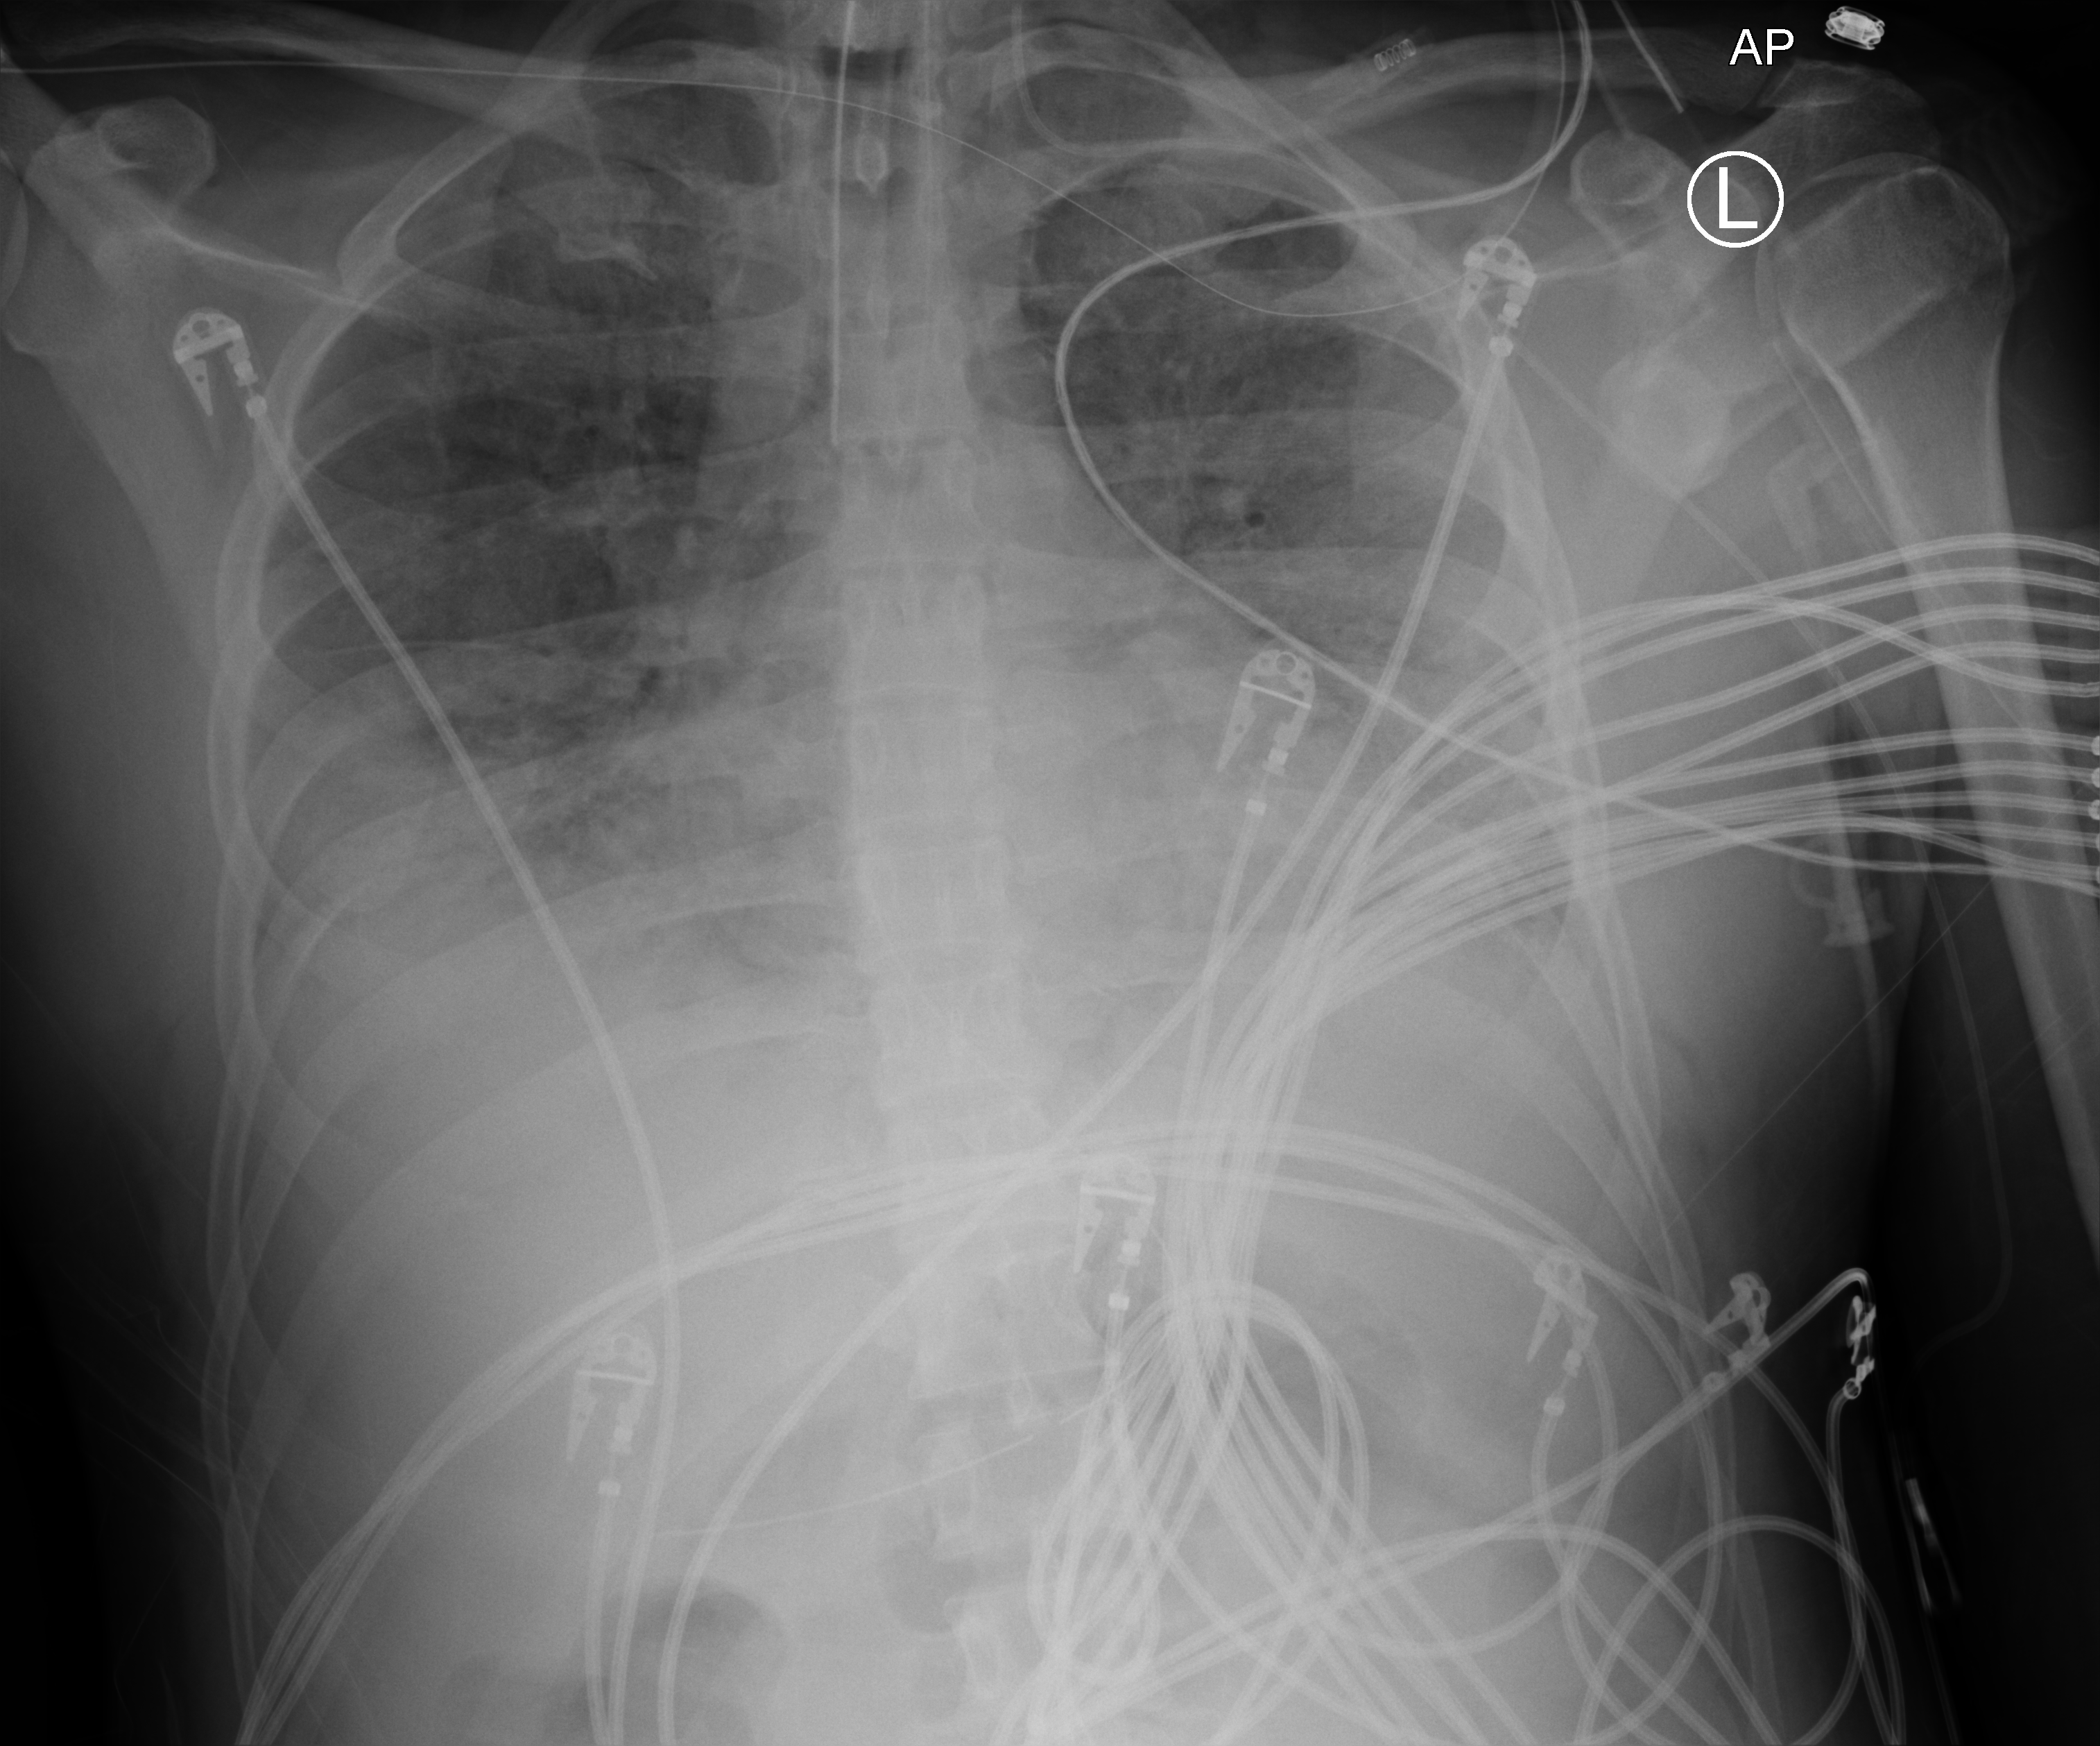
Bedside chest radiograph (computed radiography); anteroposterior (AP) projection. Patient hospitalised with COVID-19; male, aged 18–59 years.
From the hospital-stay record, not from the radiograph (when in the stay this image was taken is not recorded):
- admitted to intensive care during this hospital stay: yes